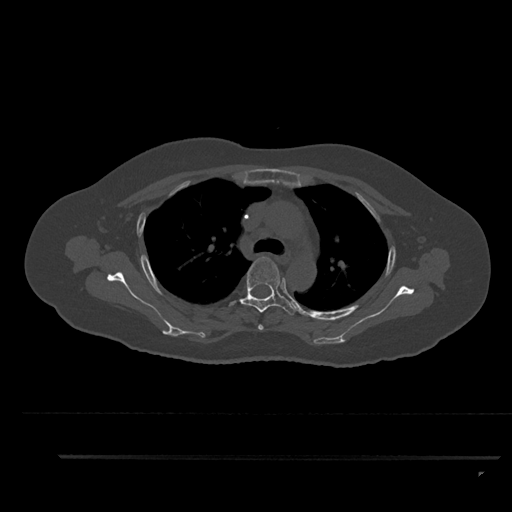
CT including the spine, one axial slice; reconstruction kernel Br40s/3; bone window (W 1800 / L 400 HU); 0.5 mm slice thickness; 512 × 512 image matrix, field of view 408 × 408 mm. Female patient, age 44 years. Case-level facts recorded for this patient, not image findings: primary cancer: renal; vertebrae with lytic lesions (as recorded): L1.
Structures marked on this image (semi-automatically segmented with operator editing):
- T3 vertebra: box from (x=258, y=324) to (x=264, y=330) px
- T4 vertebra: (x=229, y=257)–(x=296, y=315)